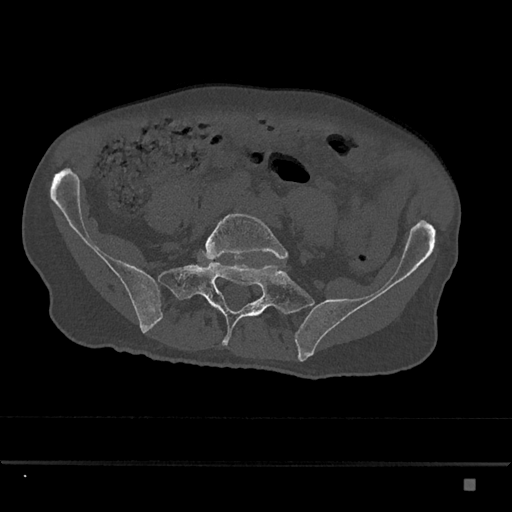
CT including the spine, one axial slice. Slice 242 of 797 in the series (ordered by position). 120 kVp. Bone window (W 1800 / L 400 HU). 0.5 mm slice thickness. 512 × 512 image matrix. Male patient, age 72 years. From the clinical record (not read from this slice): primary cancer: prostate.
Structures marked on this image (semi-automatically segmented with operator editing):
- L5 vertebra: box from (x=204, y=213) to (x=288, y=261) px